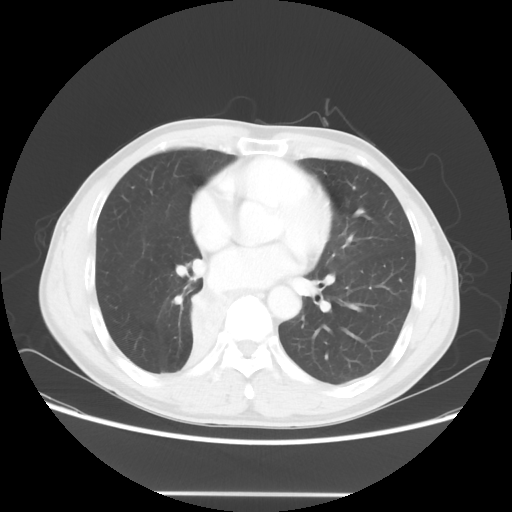
Chest CT, one axial slice. Slice 28 of 62 in the series (ordered by position). Reconstruction kernel STANDARD. Lung window (W 1500 / L -600 HU). 5 mm slice thickness. 512 × 512 image matrix, field of view 393 × 393 mm. Patient: male, 47 years. From the clinical record (not read from this slice): clinical TNM (as recorded): T2 N0 M0.
Outlined on this slice (bounding box drawn by a radiologist):
- lung tumour (recorded histology: squamous cell carcinoma): bounding box <187,285,237,348> (left, top, right, bottom; pixels)